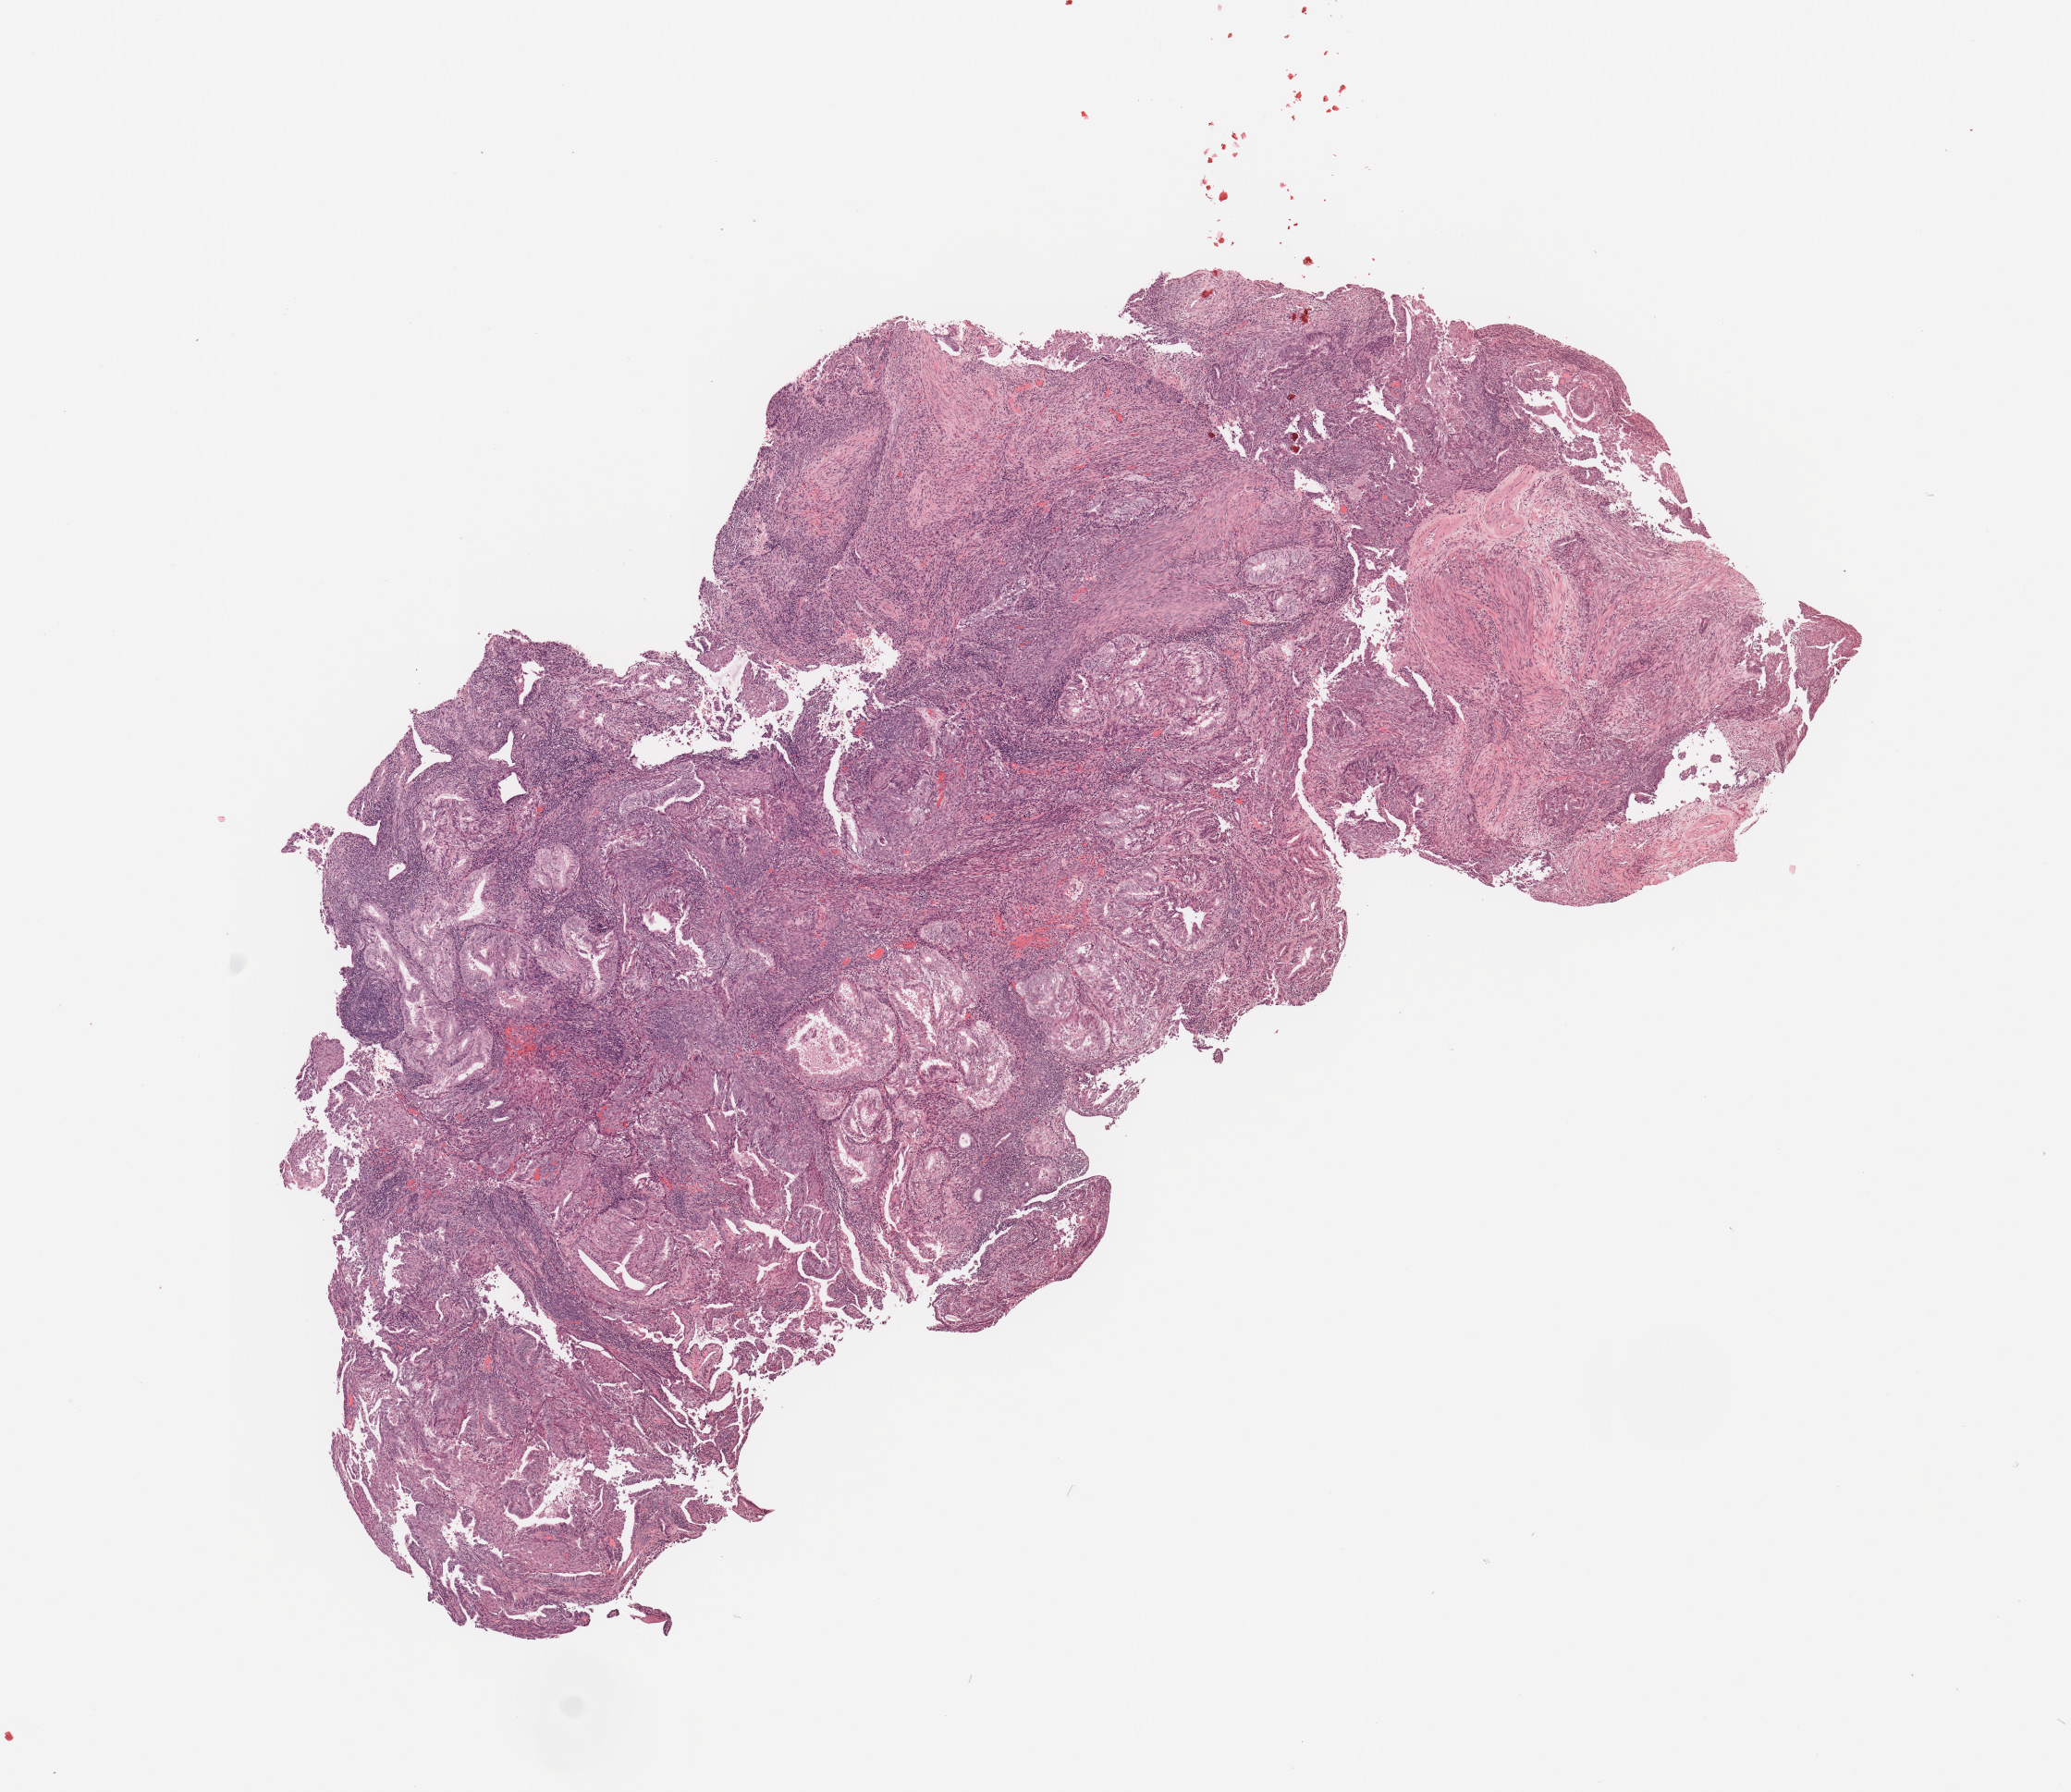
H&E-stained whole-slide image, low-resolution overview of the scanned area, about 8.9 x 7.7 mm. Tumour tissue sample, sampled site: uterus. Female, 63 y/o. Histologic grade: G1 (well differentiated). Slide review estimates, as recorded: tumour nuclei 85%, necrosis 0%.
- AJCC pathologic stage: I
- diagnosis: Endometrioid adenocarcinoma, NOS